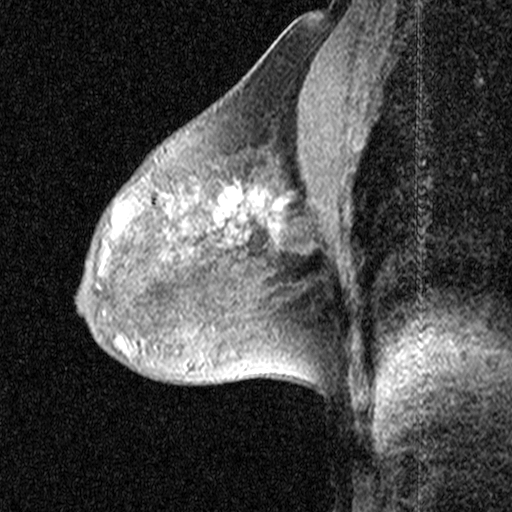
Breast MRI (dynamic contrast-enhanced), one sagittal slice; position 27 of 44 along the scan axis; dynamic contrast-enhanced study with each time point stored as its own series, time point 2 of 3 at this slice position (early post-contrast, ordered by acquisition time); 1.5 T; TE 4.5 ms, TR 11 ms; 512 × 512 image matrix. Female patient, age 53 years. Case-level facts recorded for this patient, not image findings: setting: breast cancer imaged before/during neoadjuvant chemotherapy; receptor status: HR-positive, HER2-negative.
Outlined on this slice (semi-automatically segmented with operator editing):
- analysis volume of interest (the breast-tissue region the enhancement analysis was run in; not a lesion): bounding box [x1, y1, x2, y2] px = [198, 152, 299, 267]
- tumour enhancement mask (voxels above the 90 % enhancement threshold inside the analysis volume of interest): [217, 189, 262, 219]